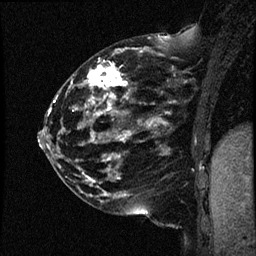
Breast MRI (dynamic contrast-enhanced), one sagittal slice. Slice 20 of 44 in the series (ordered by position). Dynamic contrast-enhanced study with each time point stored as its own series, time point 2 of 4 at this slice position (early post-contrast, ordered by acquisition time). 1.5 T. TE 4.2 ms, TR 17.7 ms. 2 mm slice thickness. 256 × 256 image matrix, field of view 200 × 200 mm. Patient: female, 52 years. Case-level facts recorded for this patient, not image findings: setting: breast cancer imaged before/during neoadjuvant chemotherapy; receptor status: HR-positive, HER2-negative.
Annotated regions visible in this slice (semi-automatic segmentation, software-assisted and operator-edited):
- analysis volume of interest (the breast-tissue region the enhancement analysis was run in; not a lesion): bounding box <47,48,163,147> (left, top, right, bottom; pixels)
- tumour enhancement mask (voxels above the 100 % enhancement threshold inside the analysis volume of interest): <80,49,163,143>